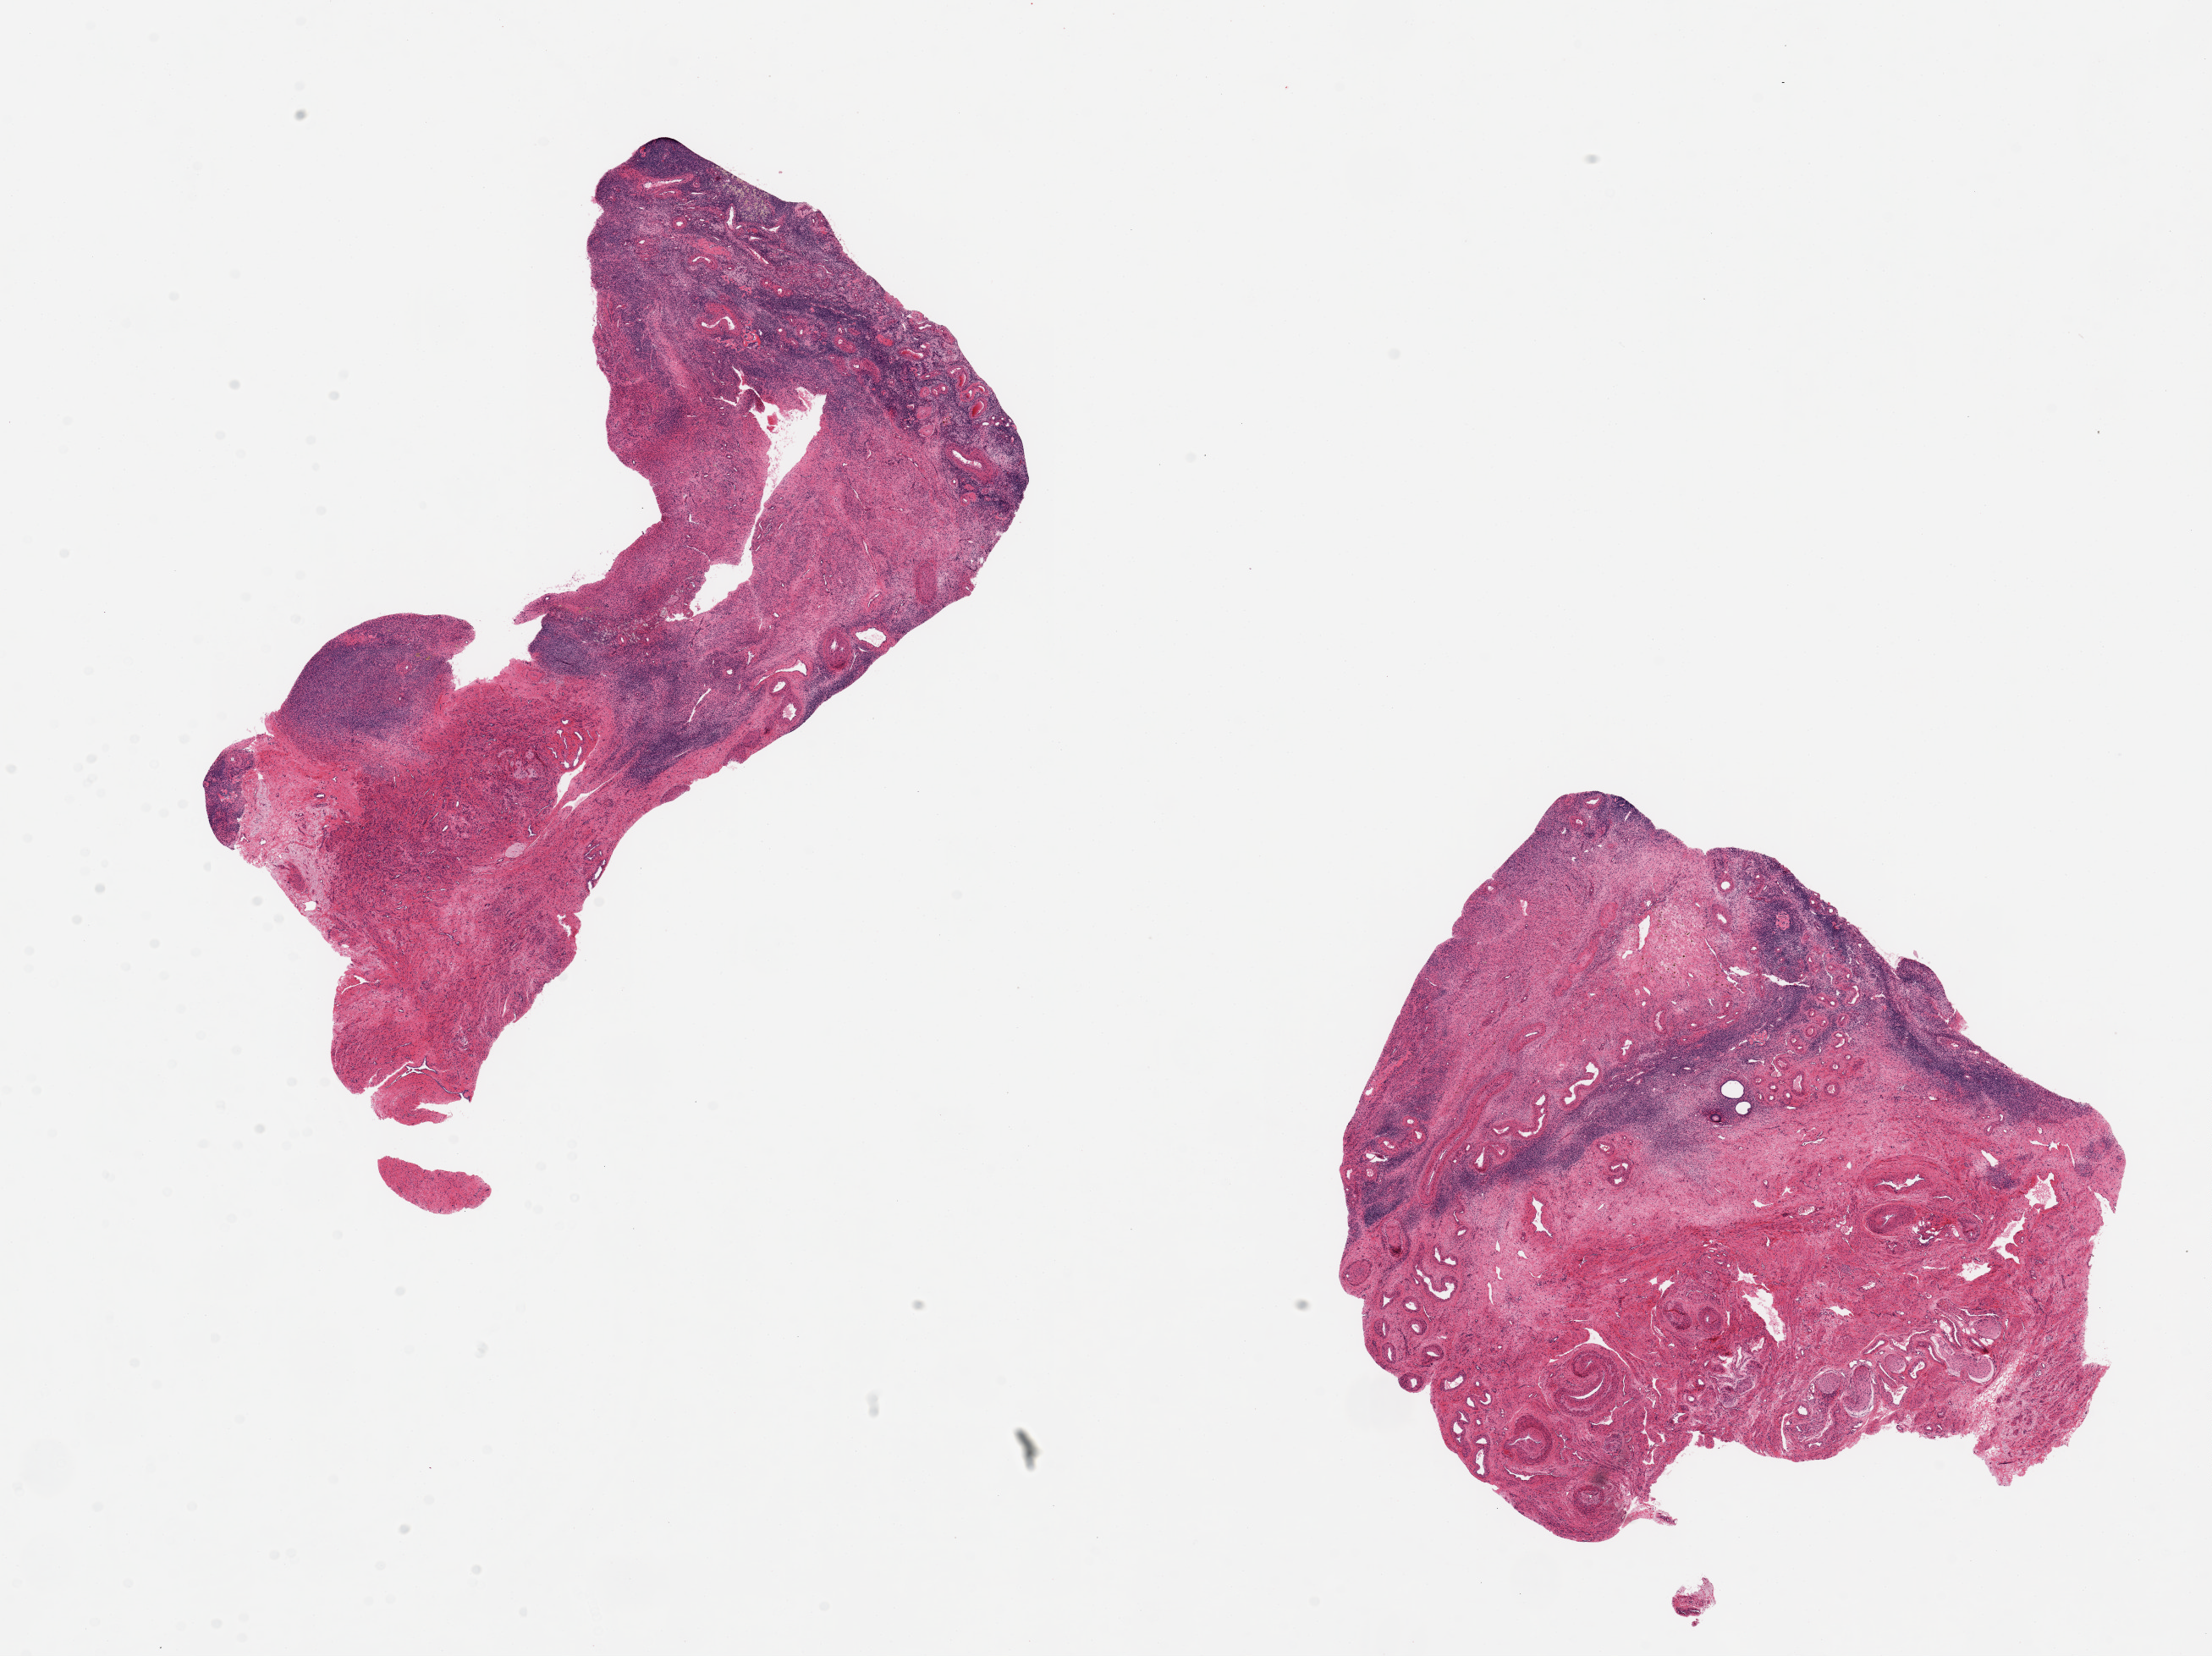
Whole-slide image, hematoxylin and eosin (H&E) stain, brightfield, a low-resolution overview of the entire scanned area, about 20.7 x 15.5 mm; PAXgene-fixed paraffin-embedded (PFPE) section; sampled site (target tissue): ovary; tissue donor sample. Female donor.
* reviewer comment on this tissue sample: 2 pieces 8x5 & 7x6 mm; very little ovarian tissue, ~ 10%